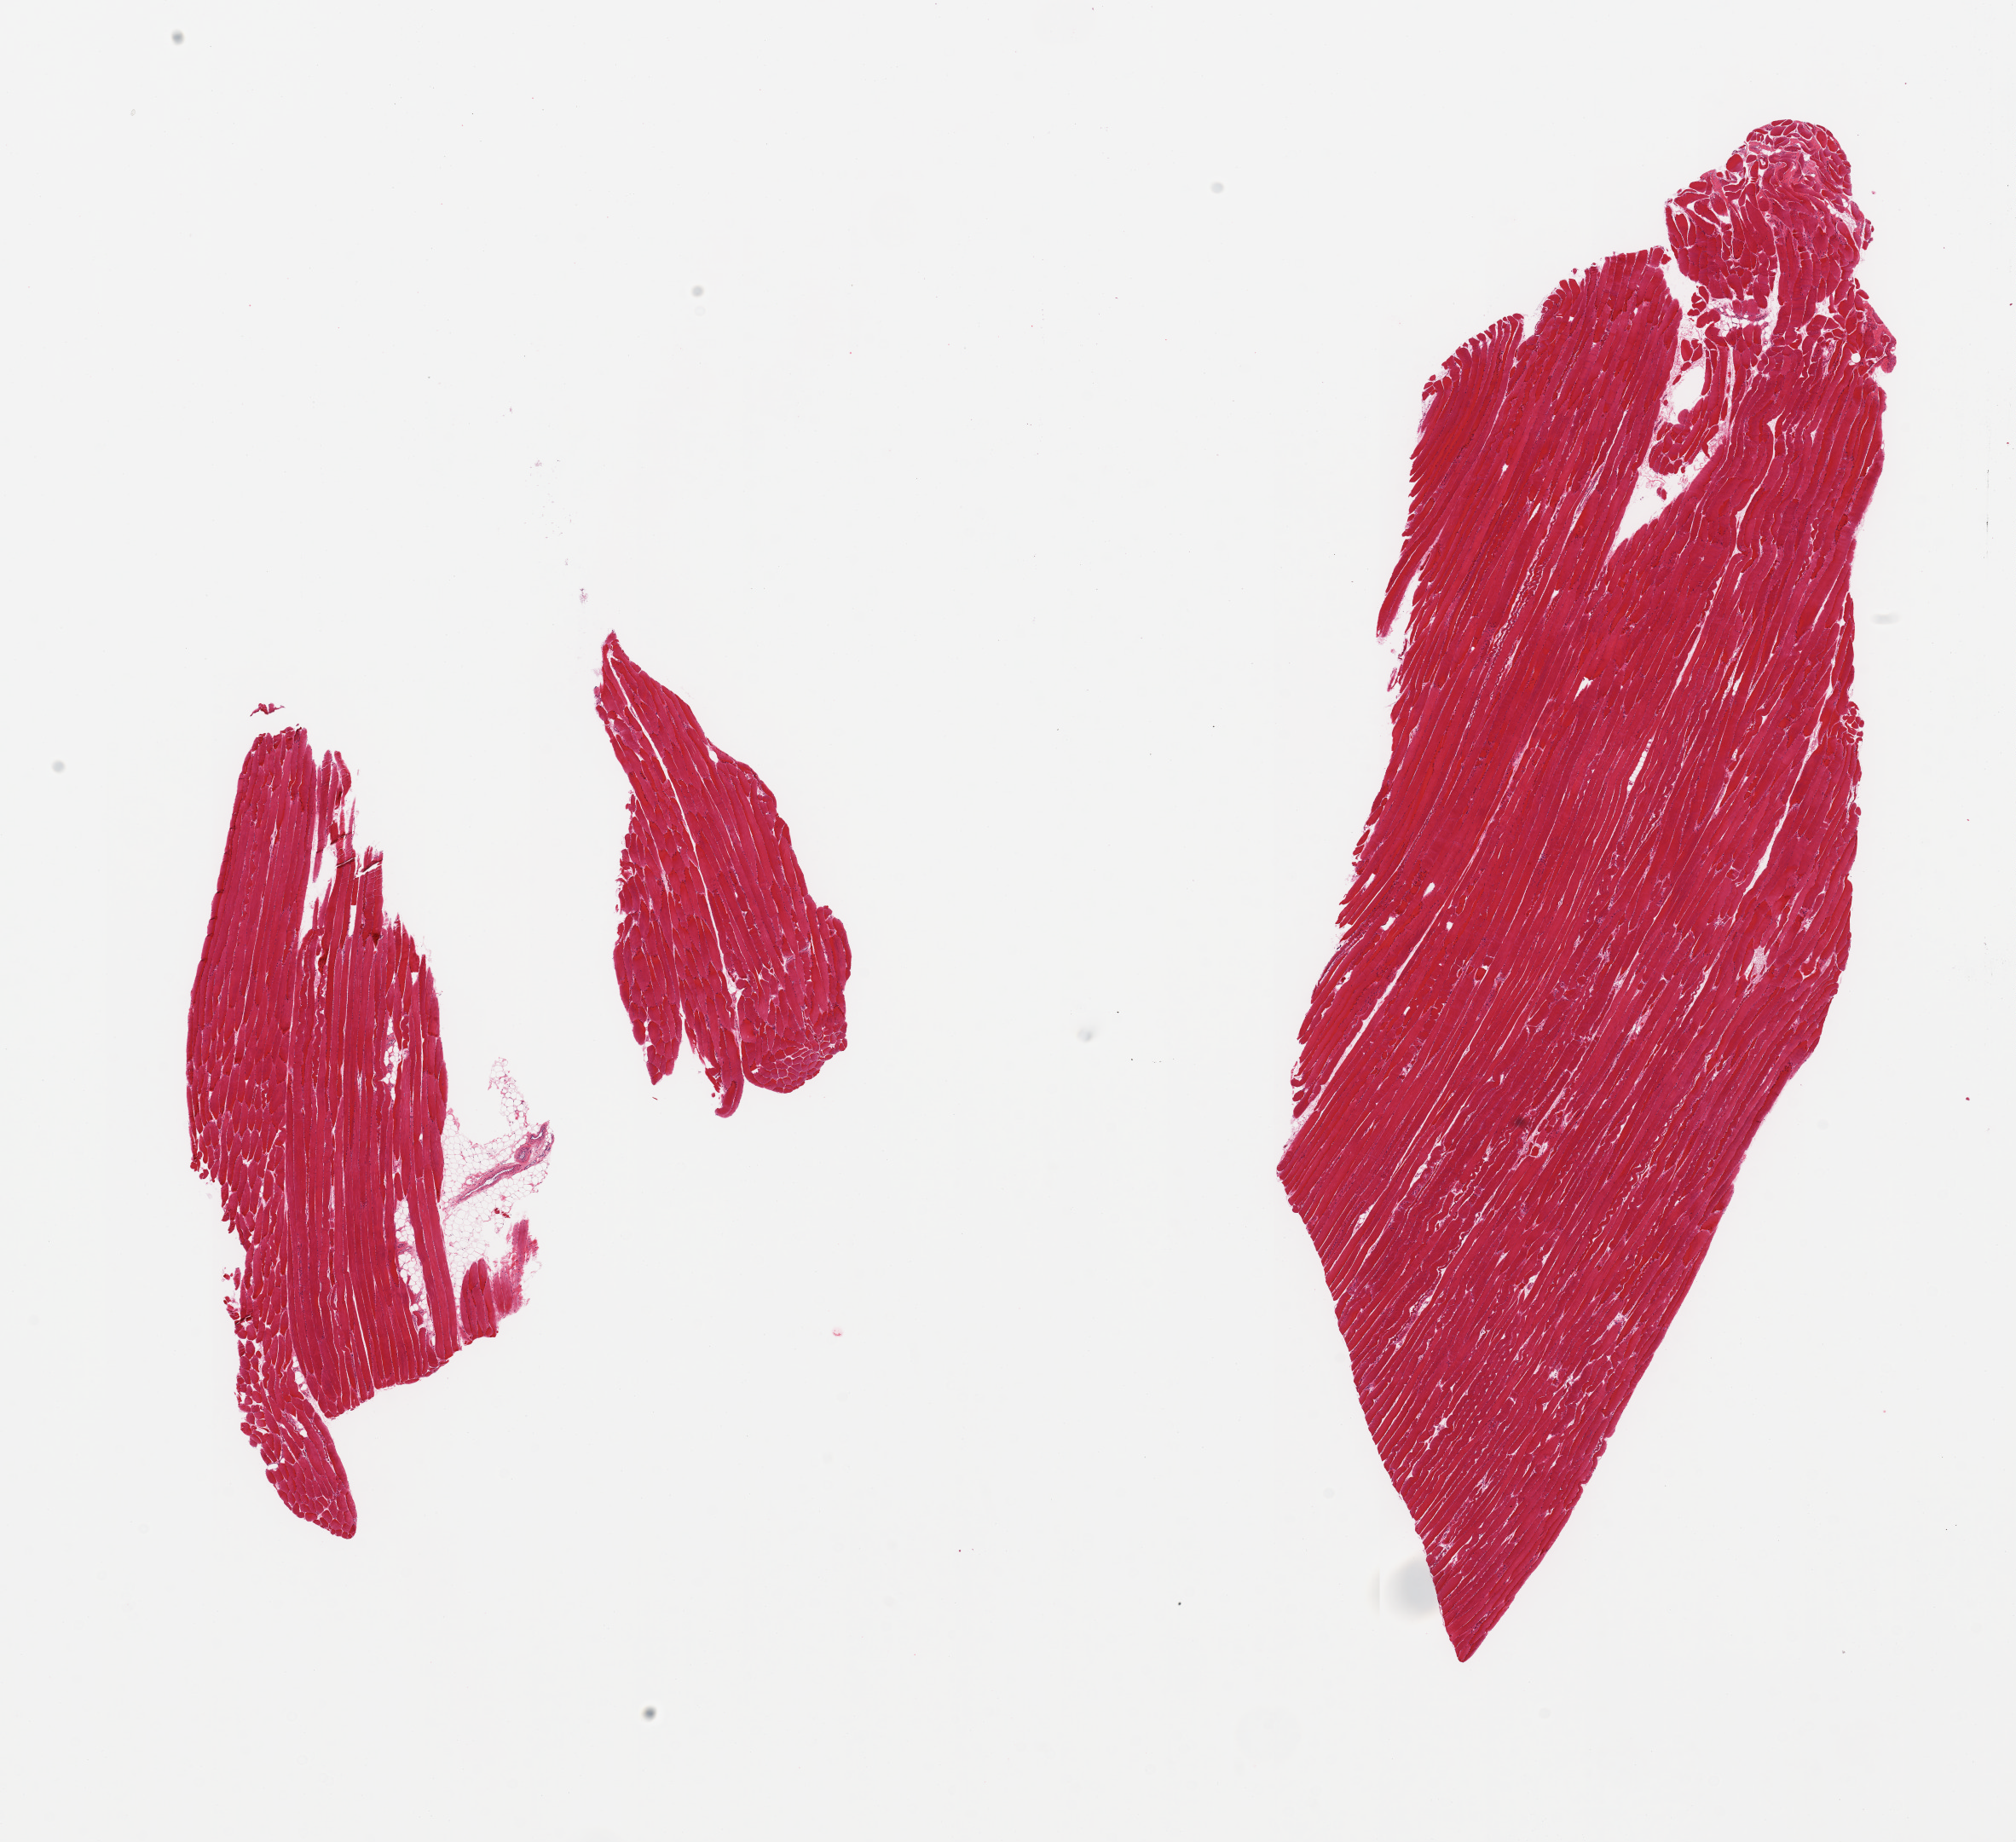
Whole-slide image, haematoxylin and eosin stain, whole scanned area (about 18.7 x 17.1 mm, from a 20x scan) shown as a low-resolution overview. PAXgene-fixed, paraffin-embedded tissue. Target tissue: skeletal muscle. Tissue donor sample. Male donor.
Pathologist's review note for this sample: 2 pieces (fragmented).